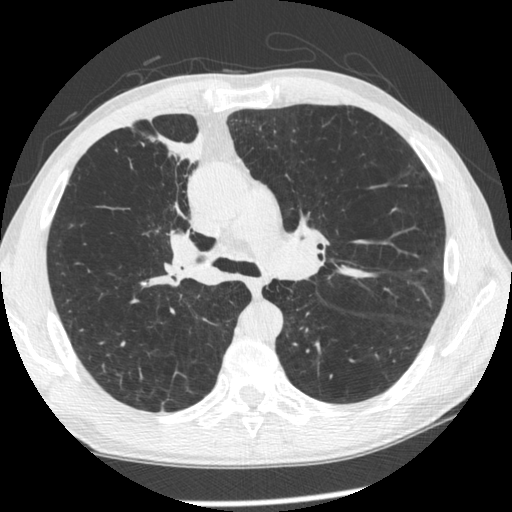
Low-dose screening chest CT, one axial slice. Position 148 of 261 along the scan axis. Reconstruction kernel STANDARD. Lung window (W 1500 / L -600 HU). 512 × 512 image matrix, field of view 340 × 340 mm.
Structures marked on this image (outlined manually by an expert reader):
- lesion 1 (tumor, upper lobe of right lung): bounding box [x1, y1, x2, y2] px = [152, 133, 205, 235]